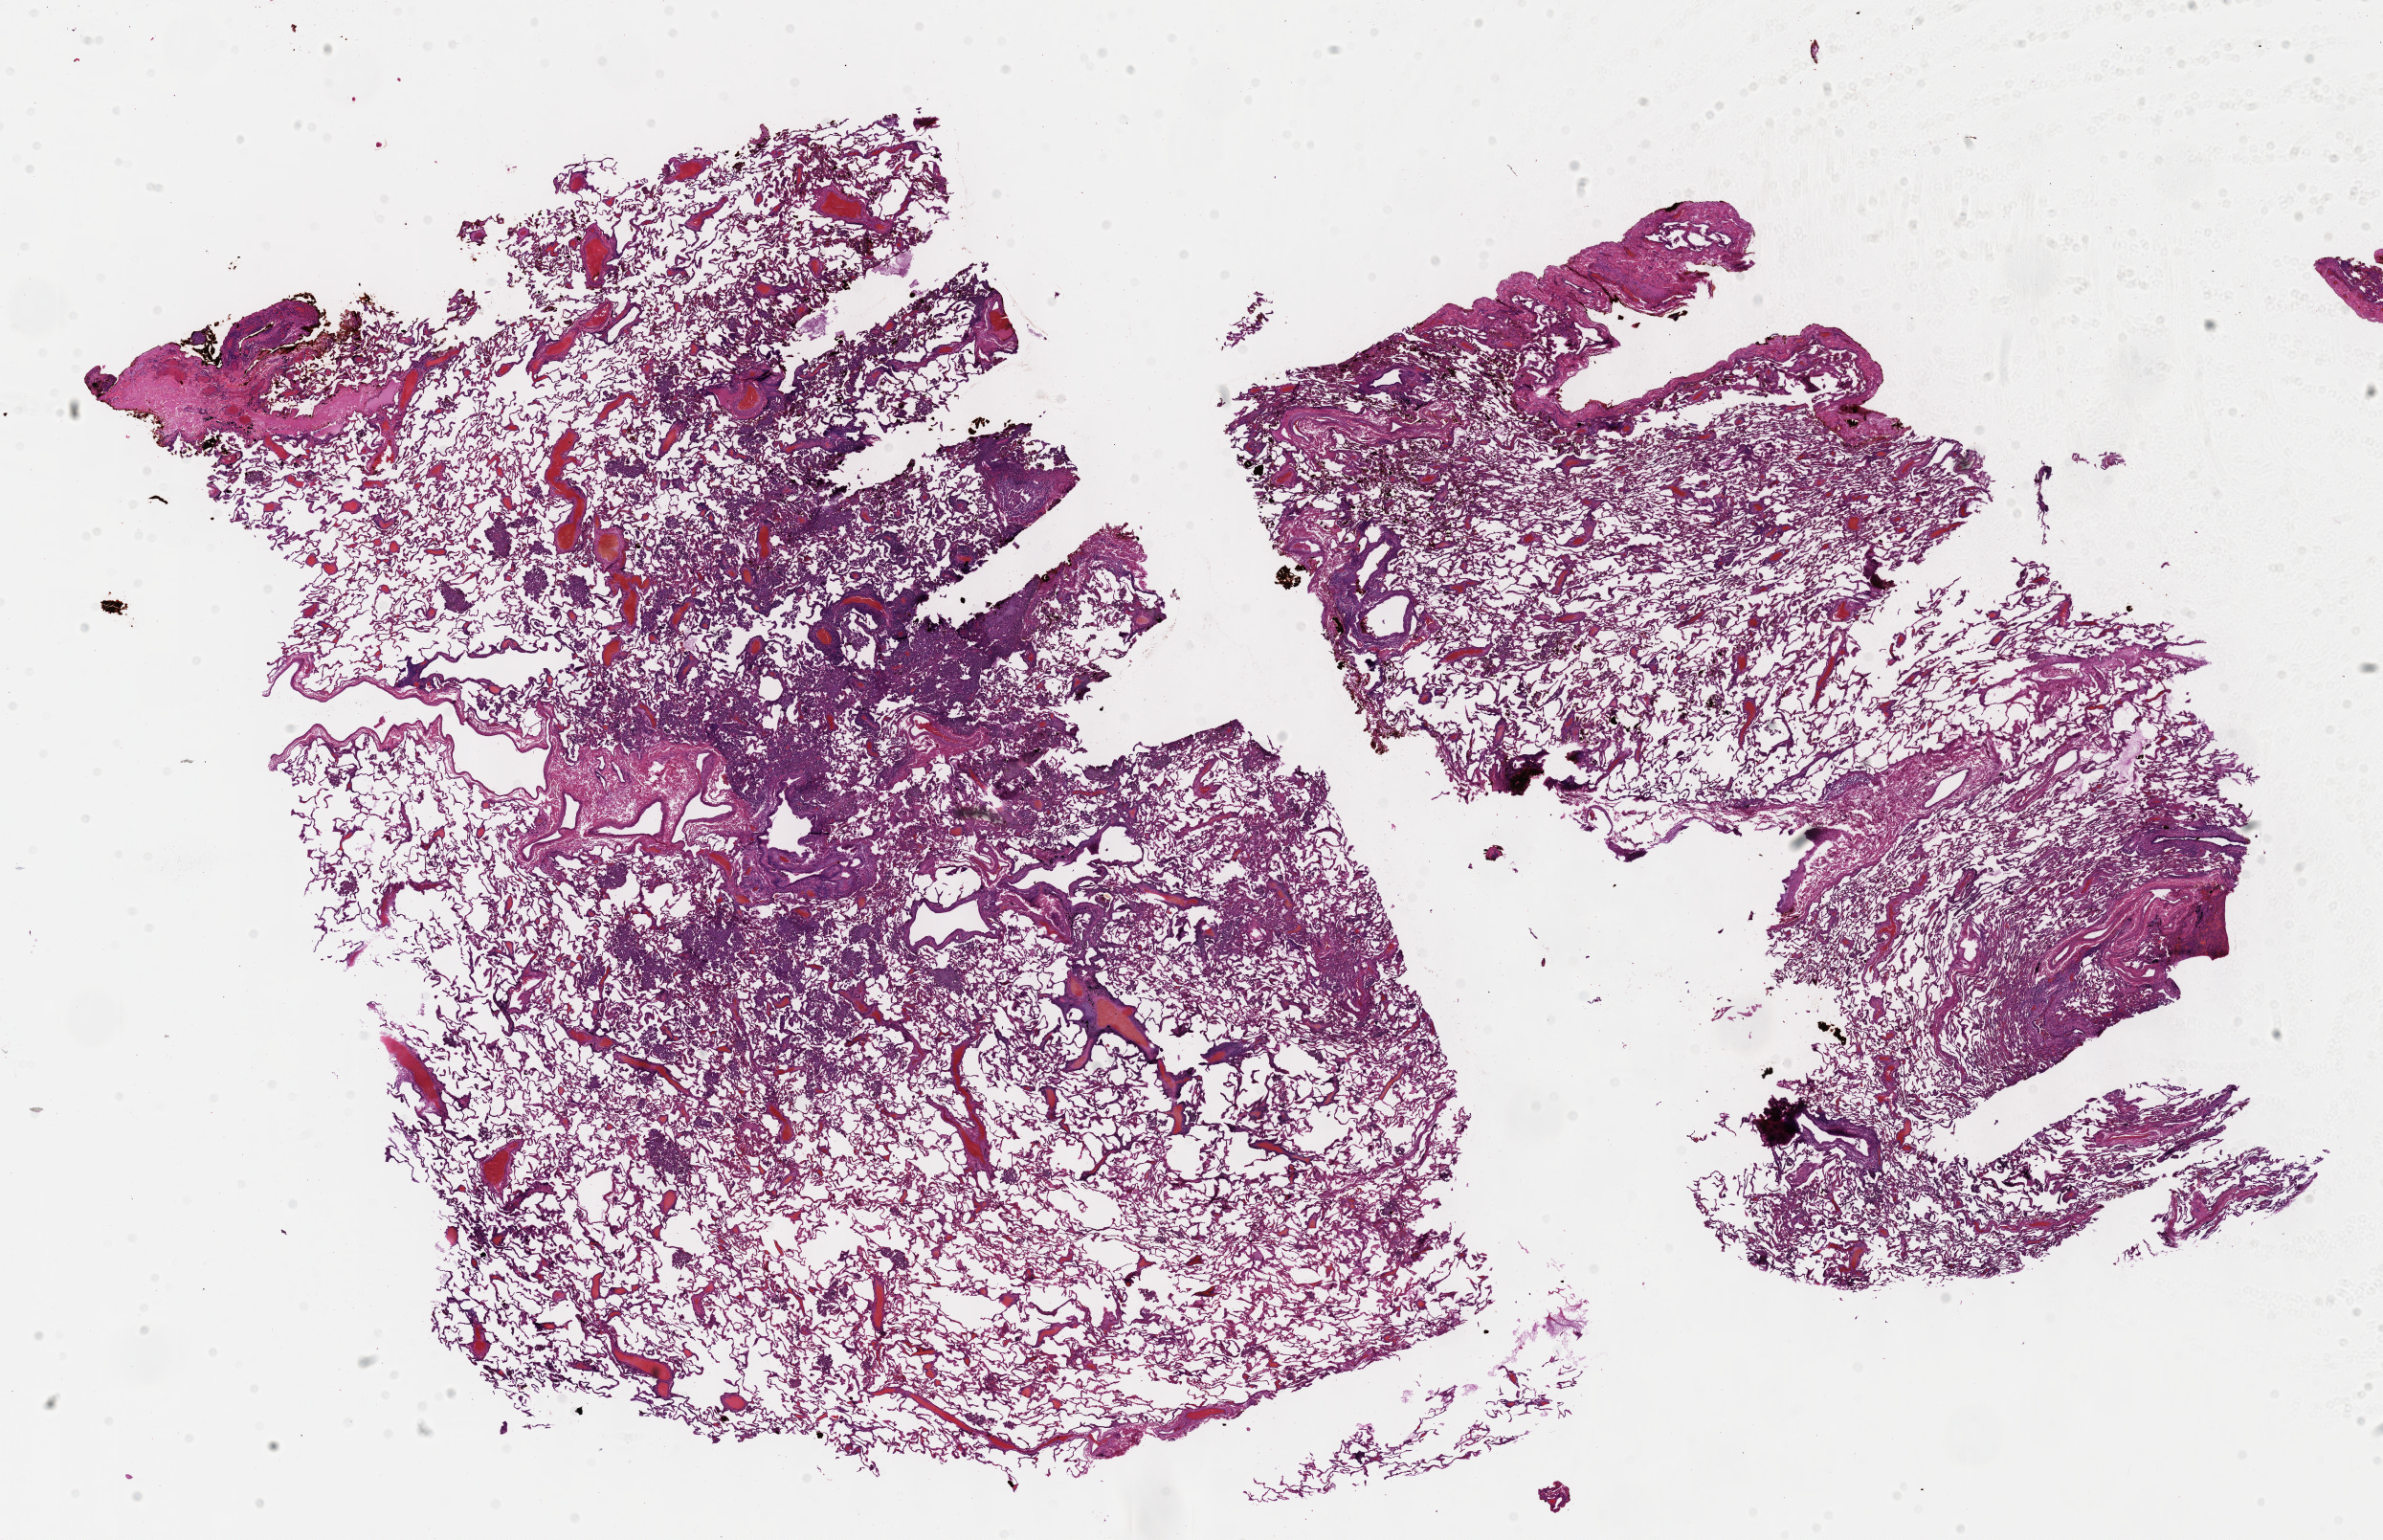
H&E whole-slide image — shown as a low-resolution overview of the whole scanned area (about 20.1 x 13.0 mm, from a 40x scan). Formalin-fixed paraffin-embedded (FFPE) diagnostic section. Primary tumour sample from the lung. Male, age 51 years at initial diagnosis.
• TNM: T2 N2 MX
• AJCC pathologic stage: IIIA (6th edition)
• pathologic diagnosis: Adenocarcinoma, NOS (upper lobe, lung)